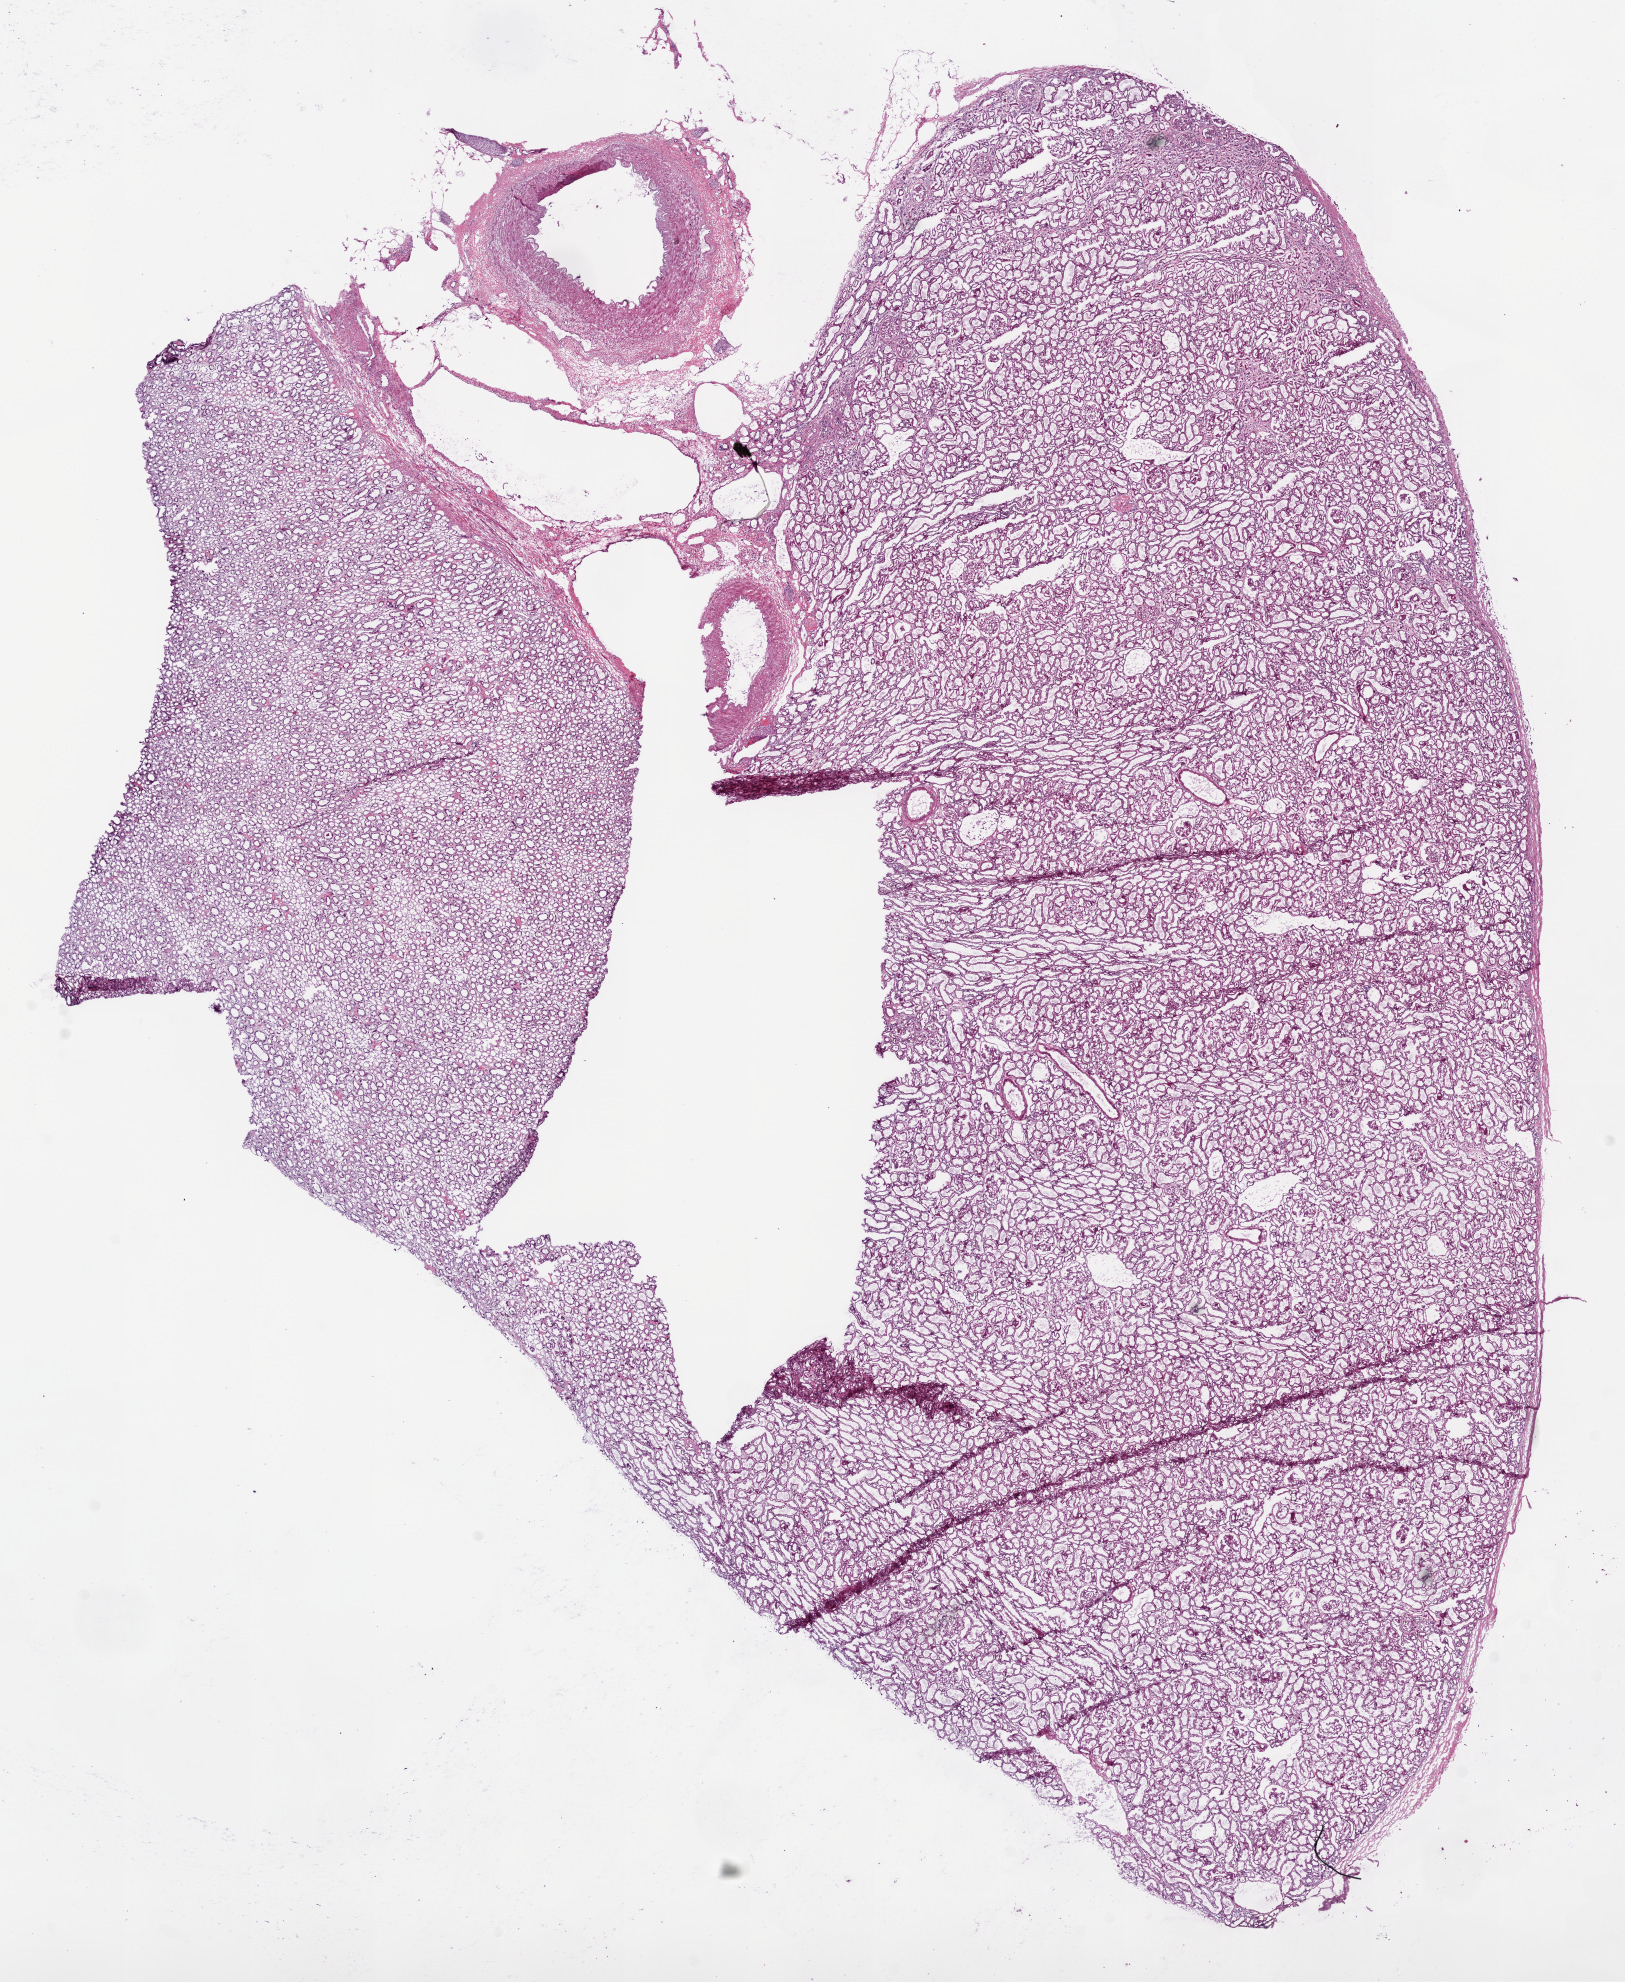
Digitized Hematoxylin and eosin (H&E) stained tissue section (whole slide), shown as a low-resolution overview of the whole scanned area (about 13.0 x 15.9 mm); frozen section; sample: solid tissue normal (non-tumour tissue), kidney. Patient: male, age at initial diagnosis 43 years.
This section: solid tissue normal sample (biorepository sample class). Patient diagnosis: Clear cell adenocarcinoma, NOS.